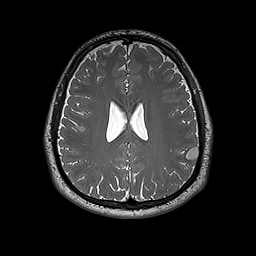
Brain MRI from a brain-tumour surgery series, one axial slice; slice 76 of 192 in the series (ordered by position); 1 mm slice thickness; 256 × 256 image matrix. From the clinical record (not read from this slice): histopathology: Dysembryoplastic neuroepithelial tumor; WHO grade: 1; IDH mutation: no.
Structures marked on this image (outlined manually by an expert reader):
- tumour: bounding box [x1, y1, x2, y2] px = [186, 146, 199, 160]